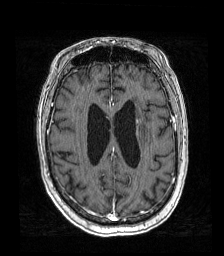
Brain MRI from a brain-tumour surgery series, one axial slice. Slice 62 of 192 in the series (ordered by position). T1-weighted post-contrast. 1 mm slice thickness. 224 × 256 image matrix, field of view 219 × 250 mm. Case-level facts recorded for this patient, not image findings: histopathology: Metastatic carcinoma from lung primary; tumour location: Left Frontal Caudate.
Outlined on this slice (expert manual segmentation):
- tumour: bounding box [x1, y1, x2, y2] px = [117, 119, 148, 134]